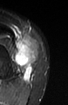
MRI of an extremity soft-tissue mass, one axial slice. Slice 24 of 52 in the series (ordered by position). STIR. MR volume resampled by the dataset authors to the PET/CT grid (not the native acquisition matrix). 3.27 mm slice thickness. 68 × 105 image matrix. Female patient. Case-level facts recorded for this patient, not image findings: histological type: spindle cell suggestive of biphasic synovial sarcoma; grade: intermediate; site of the primary tumour: left knee.
Structures marked on this image (expert contour drawn on MRI and transferred to this co-registered scan by the dataset authors):
- gross tumour volume including surrounding oedema: box from (x=14, y=40) to (x=36, y=83) px
- gross tumour volume (mass): (x=14, y=45)–(x=36, y=83)